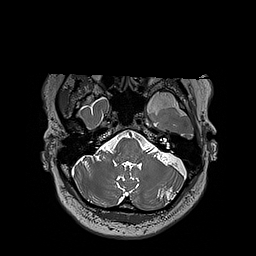
Brain MRI from a brain-tumour surgery series, one axial slice. Position 154 of 192 along the scan axis. 1 mm slice thickness. 256 × 256 image matrix, field of view 250 × 250 mm. From the clinical record (not read from this slice): histopathology: Oligodendroglioma; WHO grade: 3; IDH mutation: yes; tumour location: Left Sylvian Fissure (Temporal).
Annotated regions visible in this slice (expert manual segmentation):
- tumour: bounding box [x1, y1, x2, y2] px = [124, 91, 197, 113]